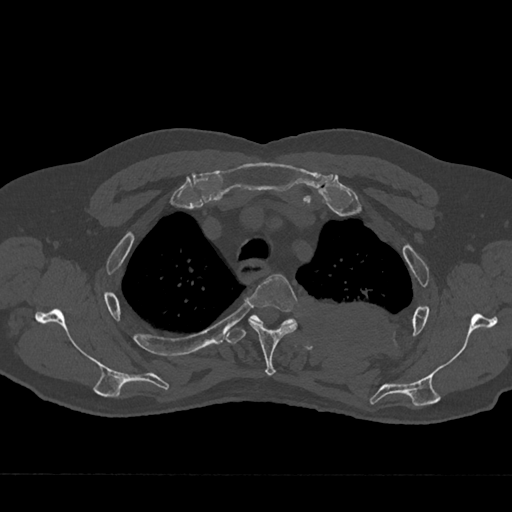
CT including the spine, one axial slice. Position 554 of 797 along the scan axis. Reconstruction kernel Br40s/3. Bone window (W 1800 / L 400 HU). 0.5 mm slice thickness. 512 × 512 image matrix, field of view 377 × 377 mm. Patient: male, 75 years. Case-level facts recorded for this patient, not image findings: primary cancer: renal.
Structures marked on this image (semi-automatic segmentation, software-assisted and operator-edited):
- T3 vertebra: bounding box (x1, y1, x2, y2) in pixels: (248, 274, 298, 376)
- T4 vertebra: (226, 314, 297, 344)